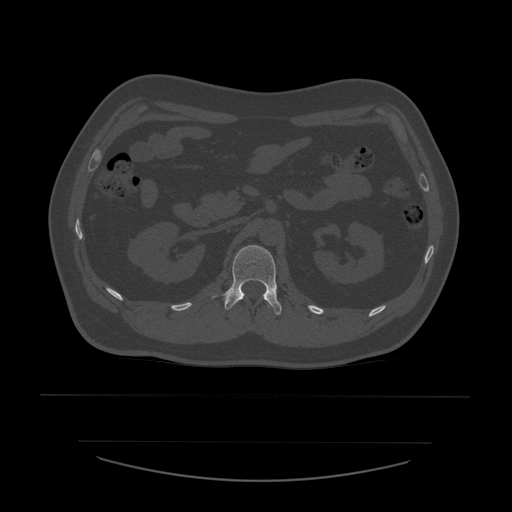
CT including the spine, one axial slice. Slice 231 of 532 in the series (ordered by position). 120 kVp. Bone window (W 1800 / L 400 HU). 1.25 mm slice thickness. 512 × 512 image matrix, field of view 441 × 441 mm. Patient age 44 years. Case-level facts recorded for this patient, not image findings: primary cancer: soft tissue sarcoma.
Annotated regions visible in this slice (semi-automatic segmentation, software-assisted and operator-edited):
- L1 vertebra: bounding box [x1, y1, x2, y2] px = [212, 245, 282, 315]